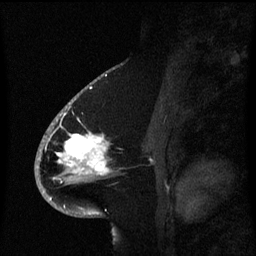
Breast MRI (dynamic contrast-enhanced), one sagittal slice. Slice 36 of 60 in the series (ordered by position). Dynamic contrast-enhanced series, image 2 of 3 at this slice position (ordered by acquisition). 1.5 T. TE 4.2 ms, TR 8.4 ms. 2.1 mm slice thickness. 256 × 256 image matrix. Patient: female, 53 years. From the clinical record (not read from this slice): setting: breast cancer imaged before/during neoadjuvant chemotherapy; receptor status: HR-positive, HER2-negative.
Annotated regions visible in this slice (semi-automatic segmentation, software-assisted and operator-edited):
- analysis volume of interest (the breast-tissue region the enhancement analysis was run in; not a lesion): bounding box <49,108,119,201> (left, top, right, bottom; pixels)
- tumour enhancement mask (voxels above the 70 % enhancement threshold inside the analysis volume of interest): <51,132,110,201>